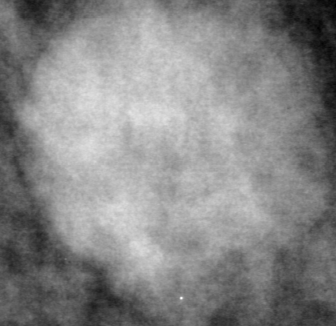
Crop from a digitized film mammogram around one marked abnormality, right breast, MLO view.
- Finding: mass, shape round, margins obscured; BI-RADS assessment category 4; pathology result (as recorded, not read from the image): benign.